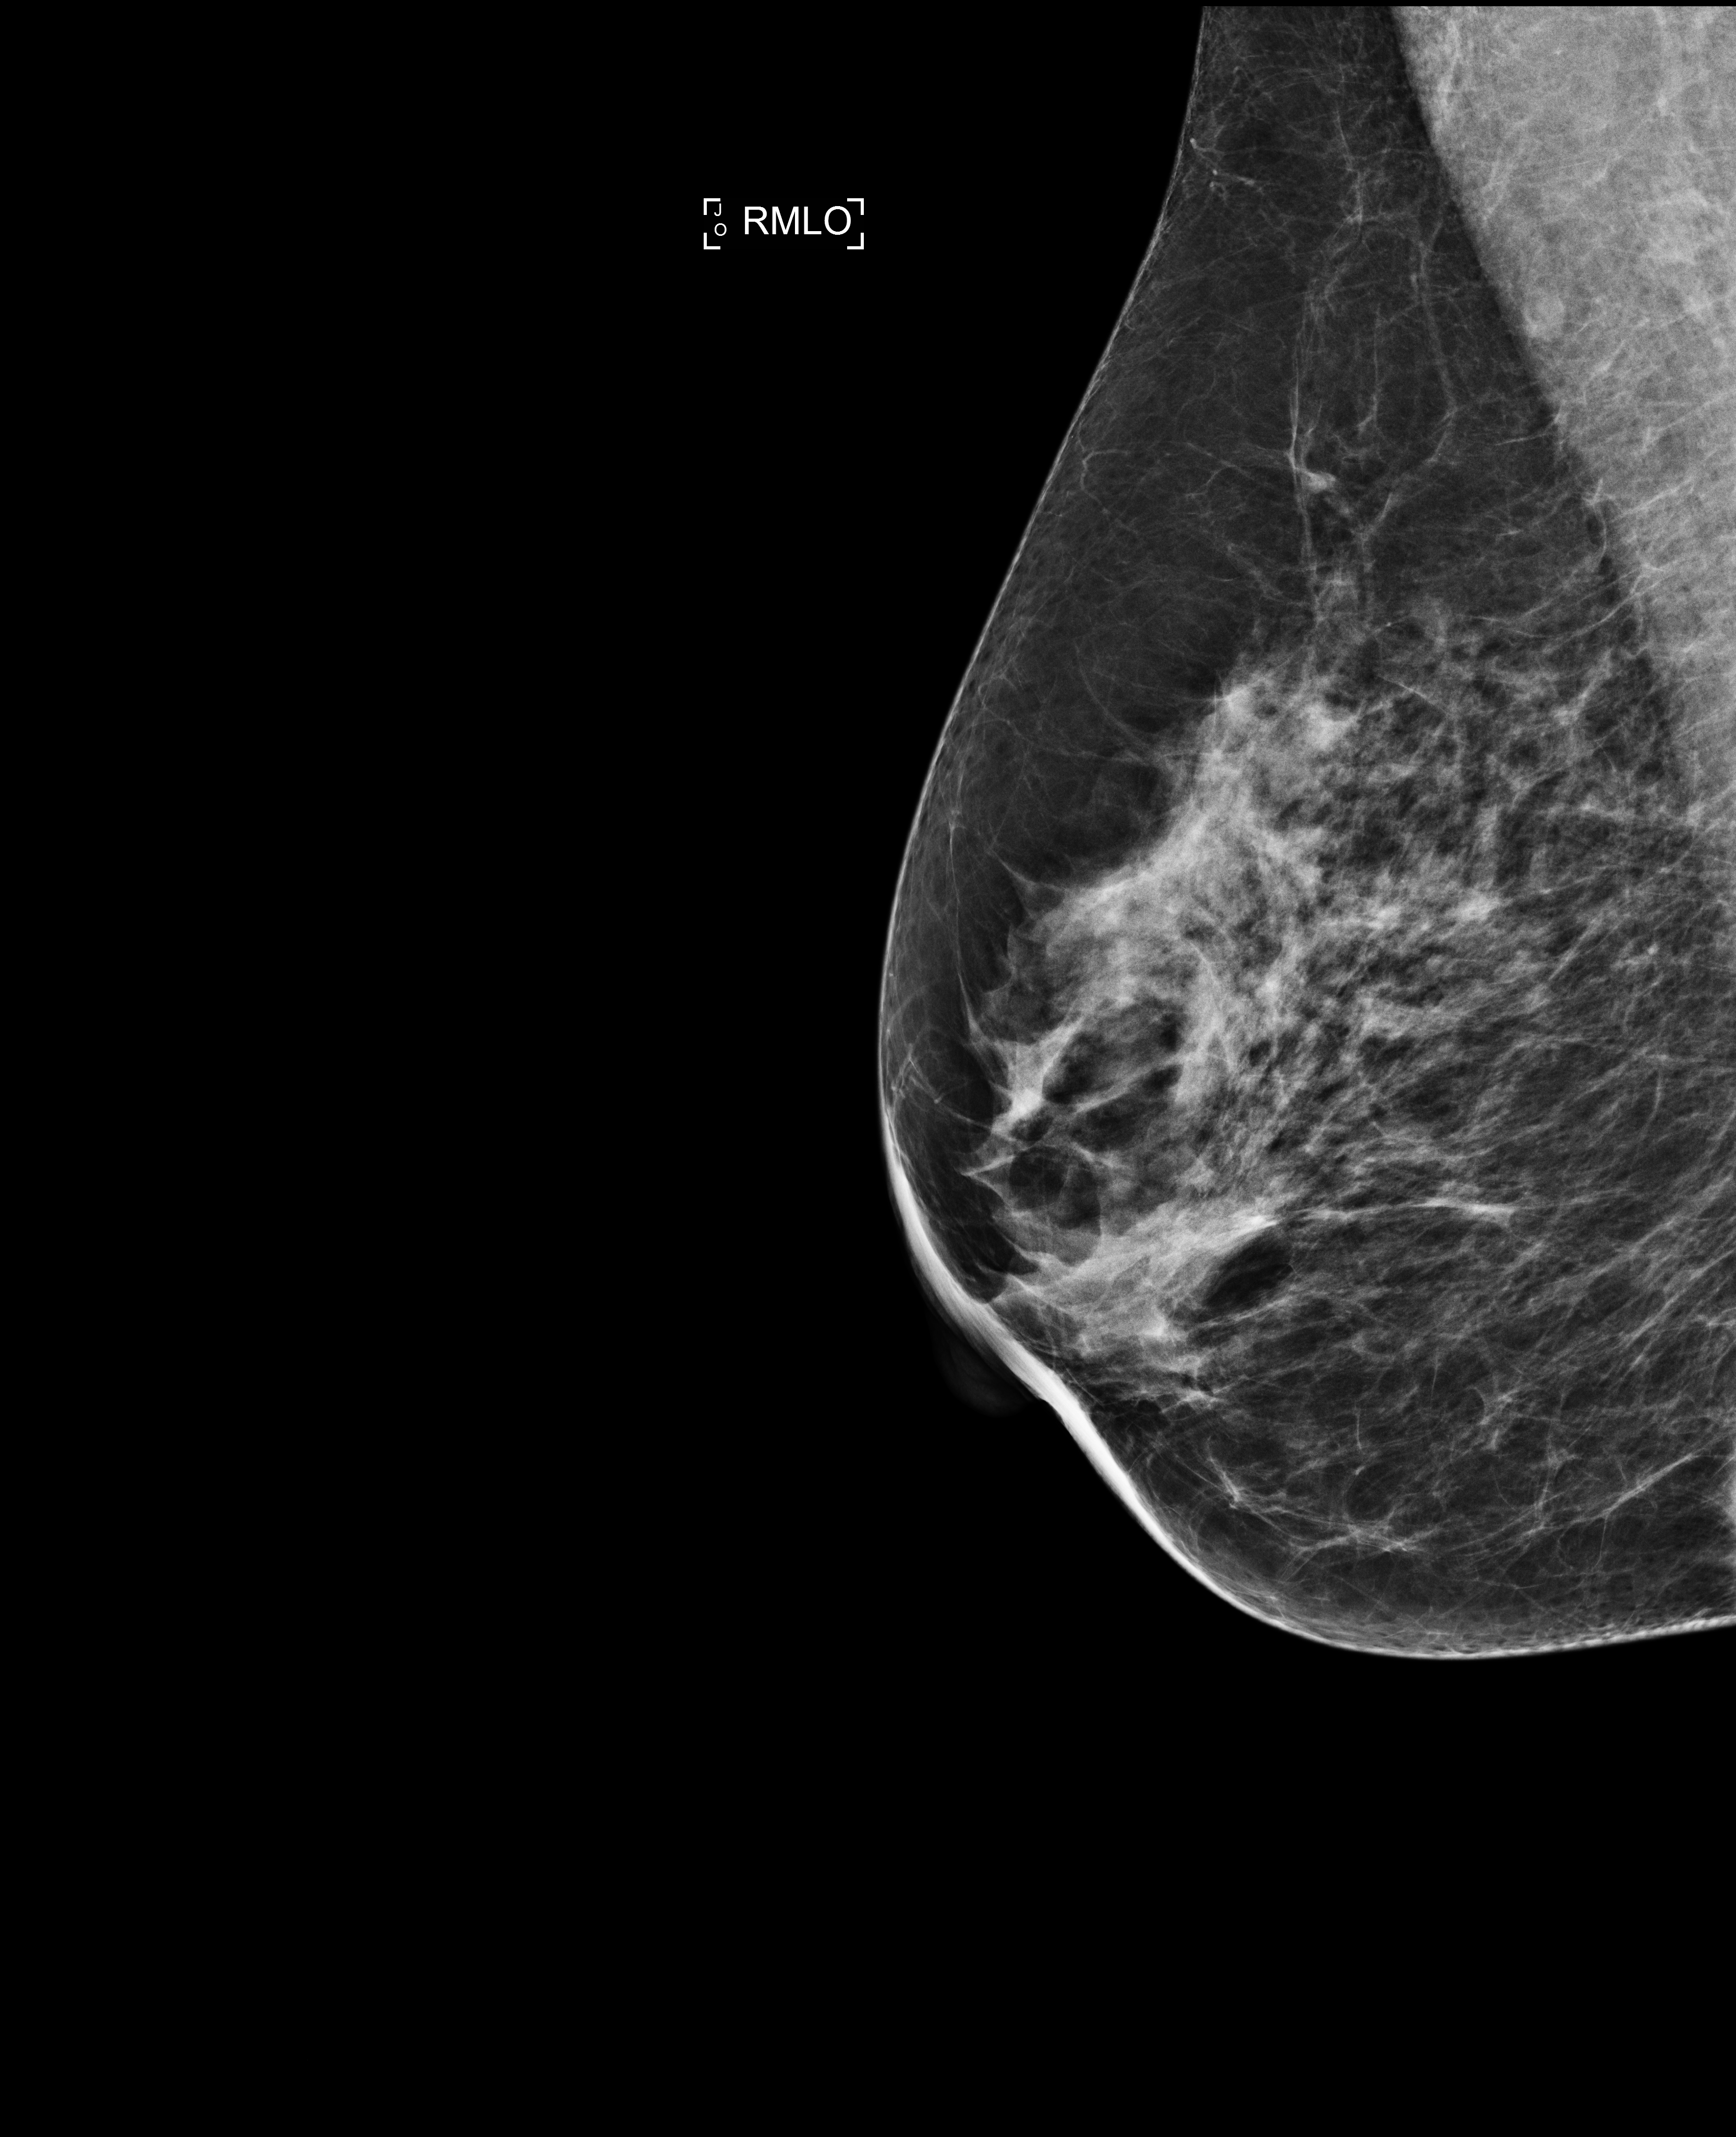
Digital mammogram (FFDM); right breast; medio-lateral oblique projection; annual screening mammography examination; compressed breast thickness 61 mm; system: Selenia Dimensions. Patient aged 57 years (female).
Final BI-RADS assessment for this screening round (tomosynthesis exam, both breasts): category 1.